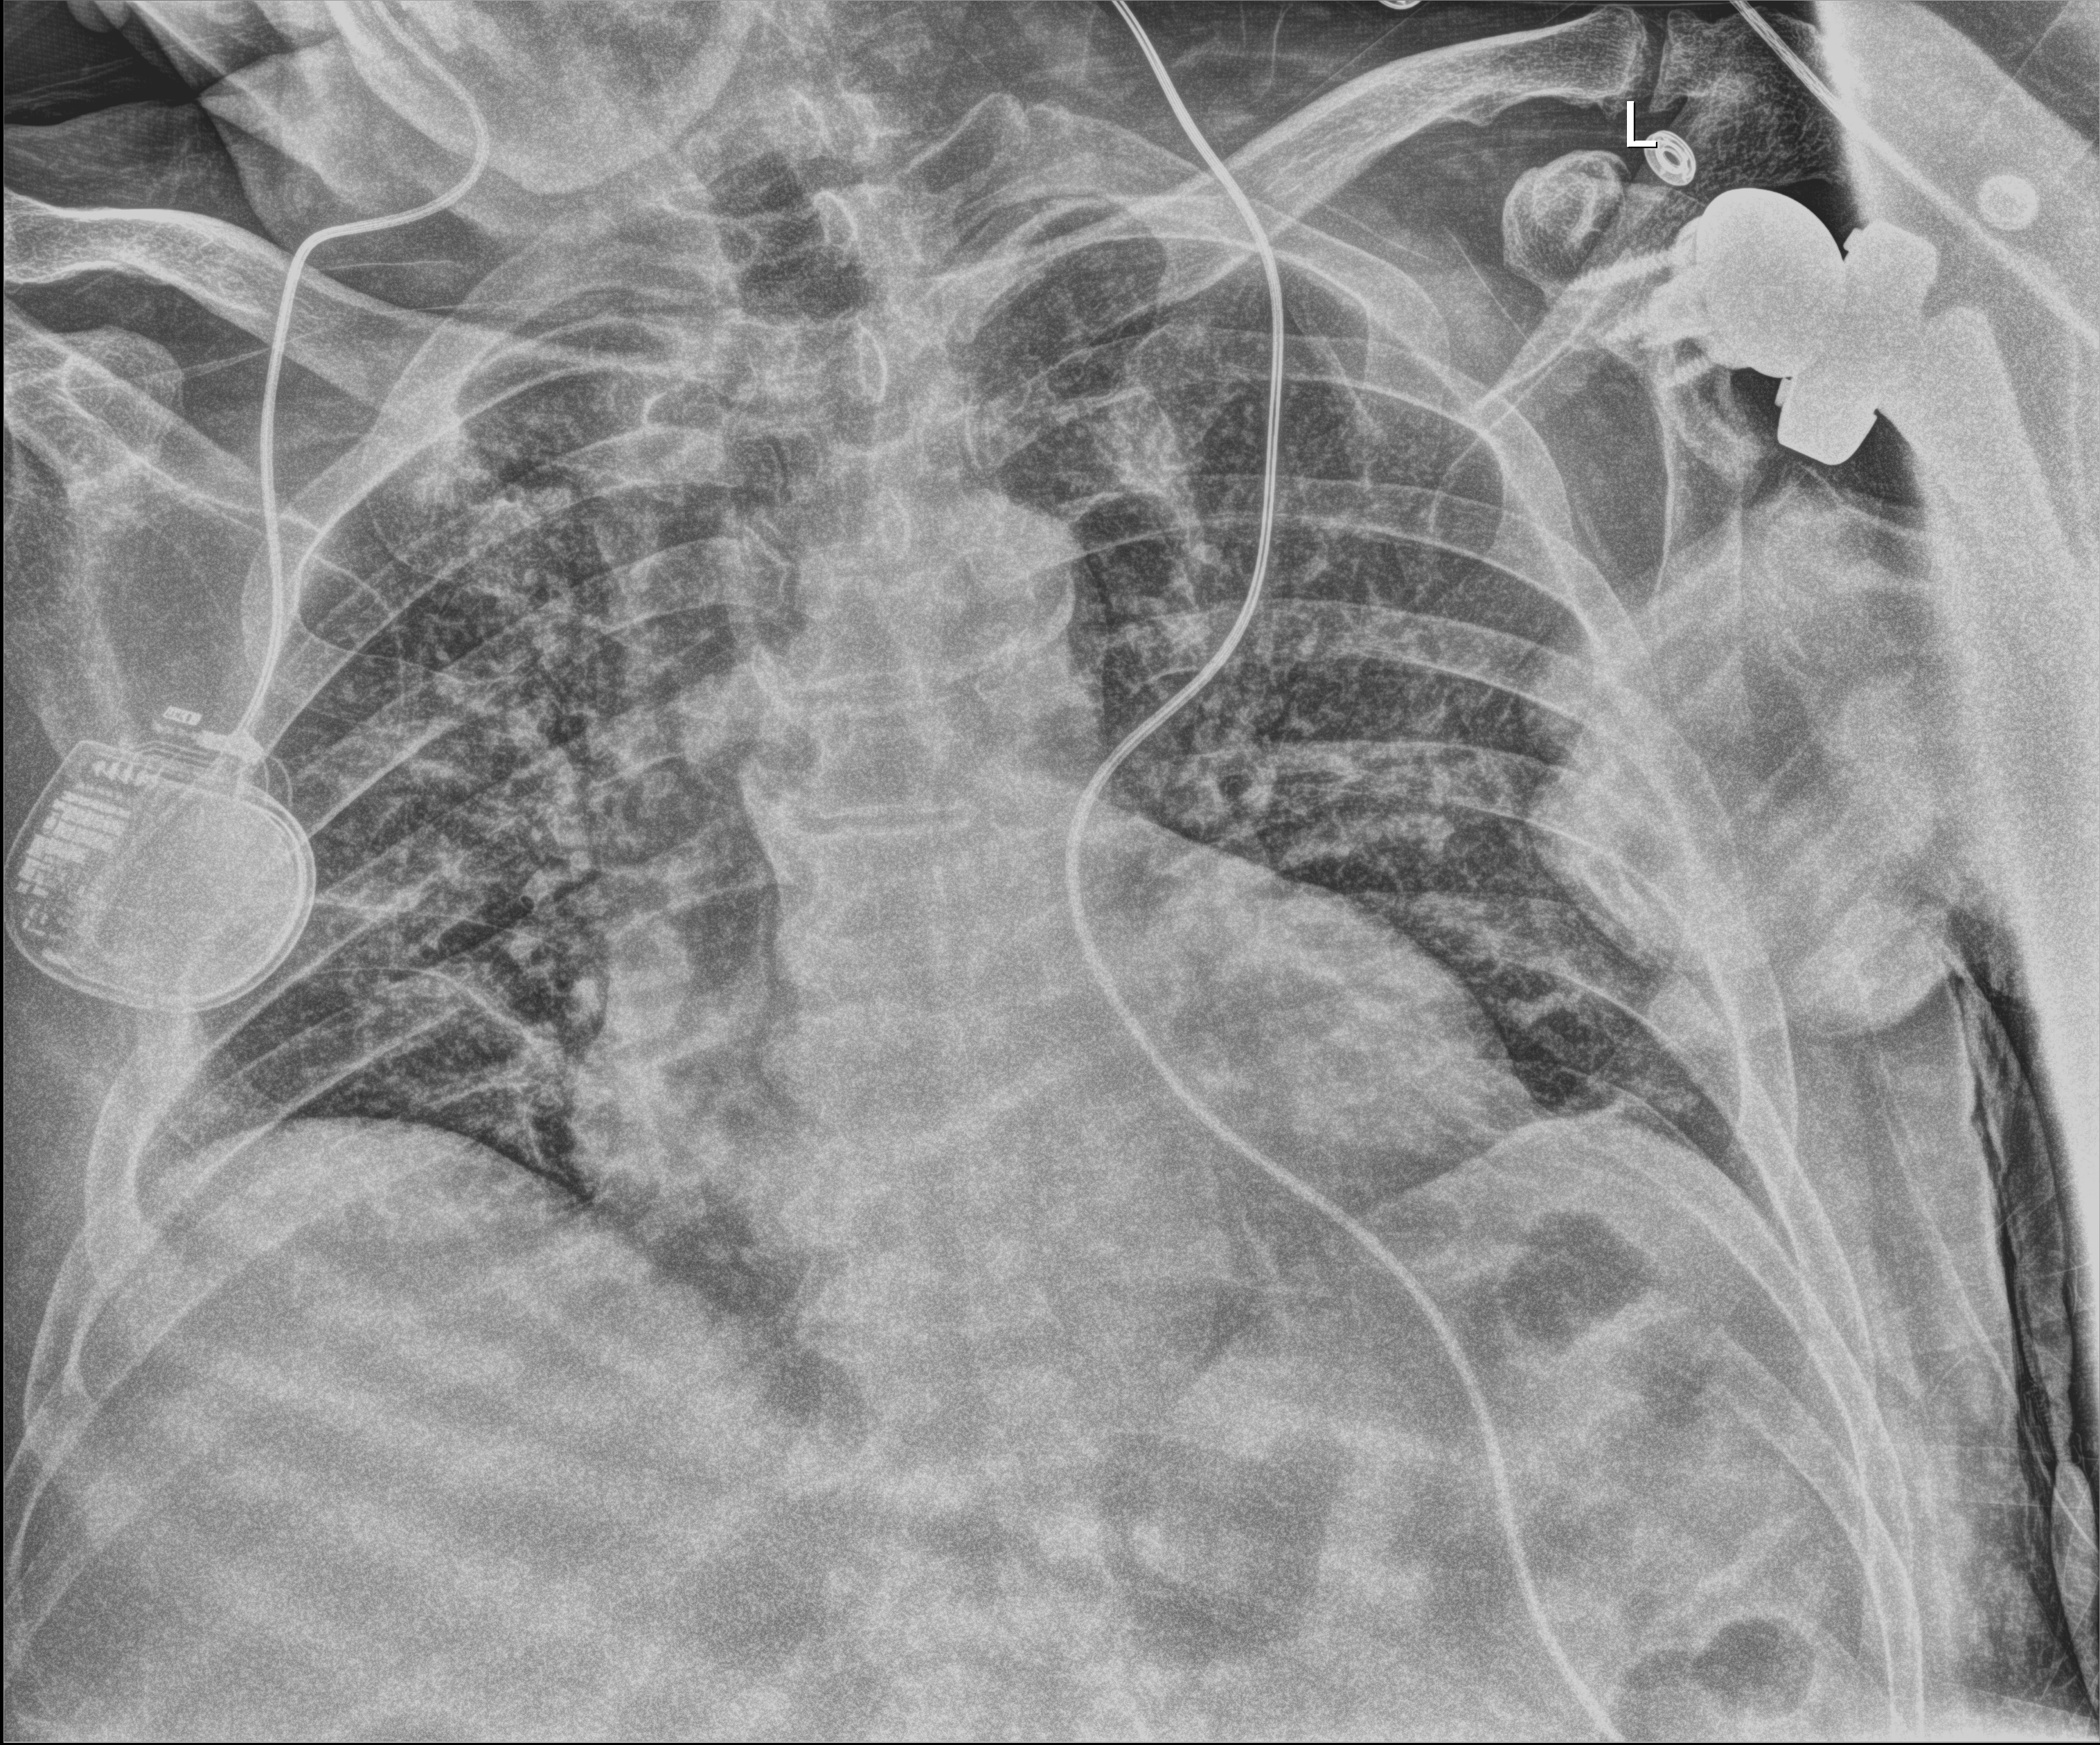
Portable chest radiograph, anteroposterior (AP) projection. Male patient hospitalised with COVID-19, age 60–74 years.
Admission-level facts for this patient (not findings on this image; timing relative to this image not recorded): mechanically ventilated during this hospital stay: no.